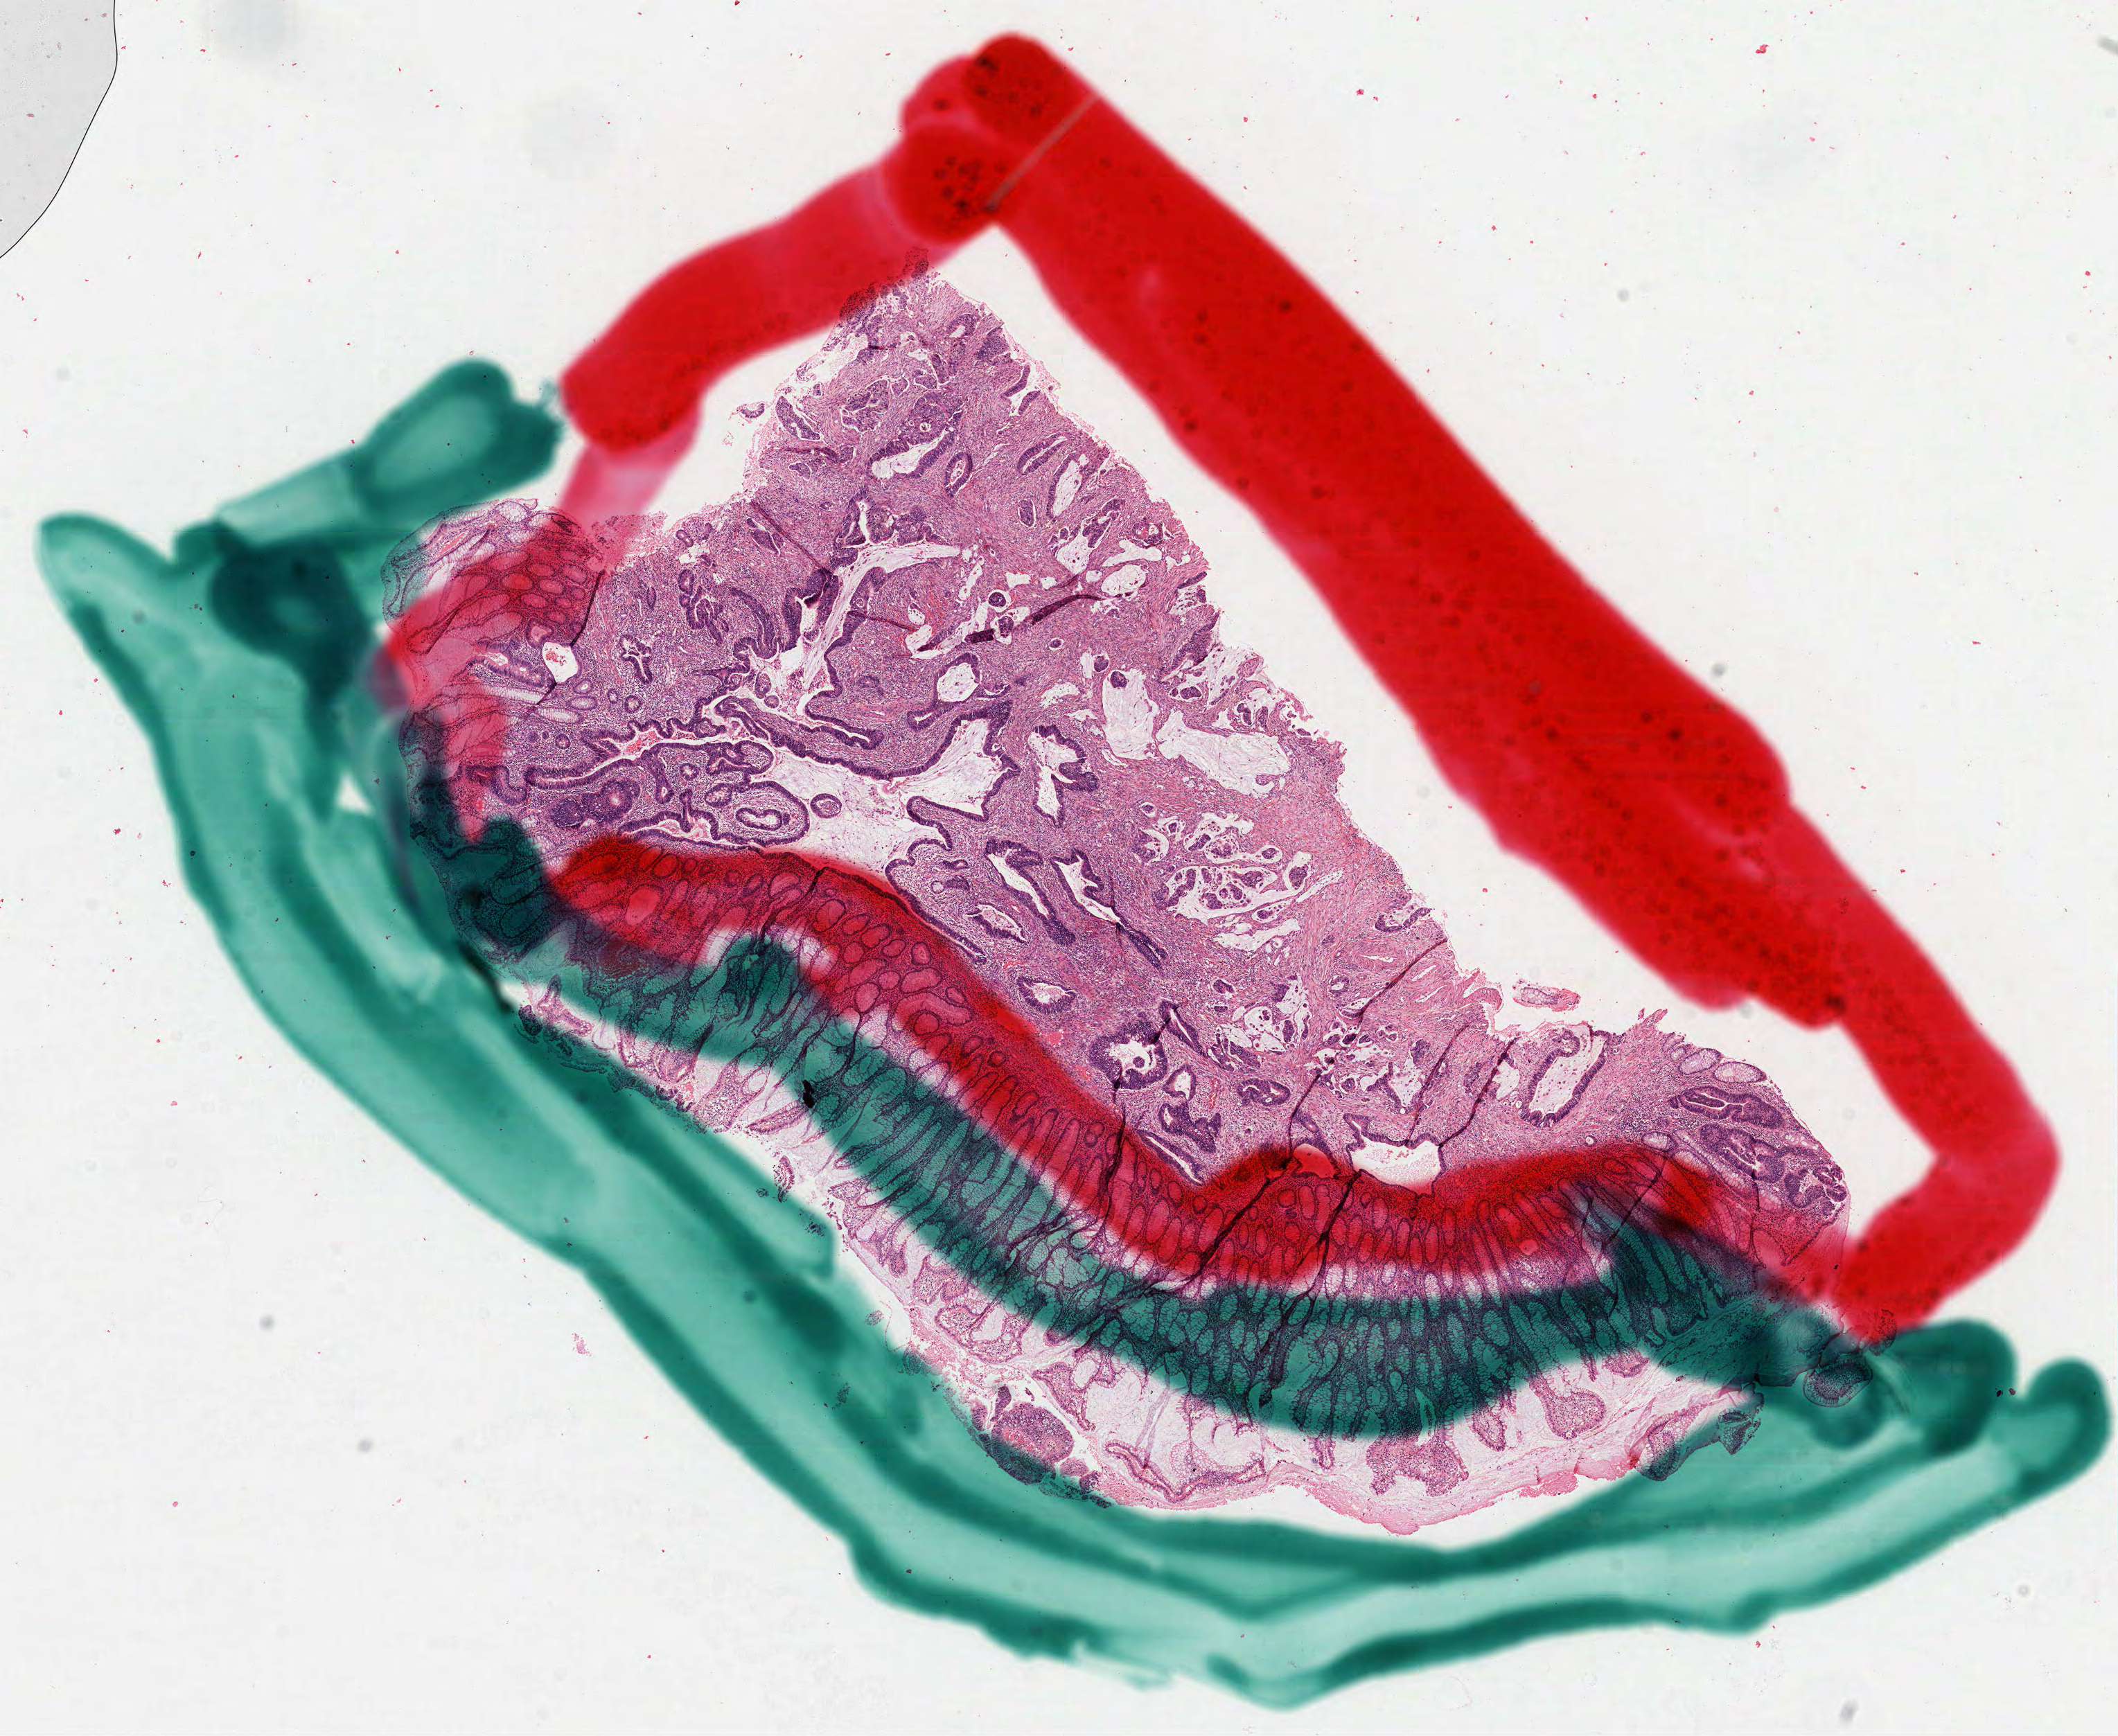
Whole-slide histology image, Hematoxylin and eosin (H&E) stained, low-resolution overview of the scanned area, about 12.3 x 10.1 mm (slide scanned at 40x); formalin-fixed paraffin-embedded (FFPE) diagnostic section; rectum, primary tumour sample. Female, age 72 years at initial diagnosis.
- pathologic diagnosis: Adenocarcinoma, NOS (rectosigmoid junction)
- lymph nodes positive (case pathology): 0 of 8 examined
- AJCC pathologic stage: IIA (7th edition)